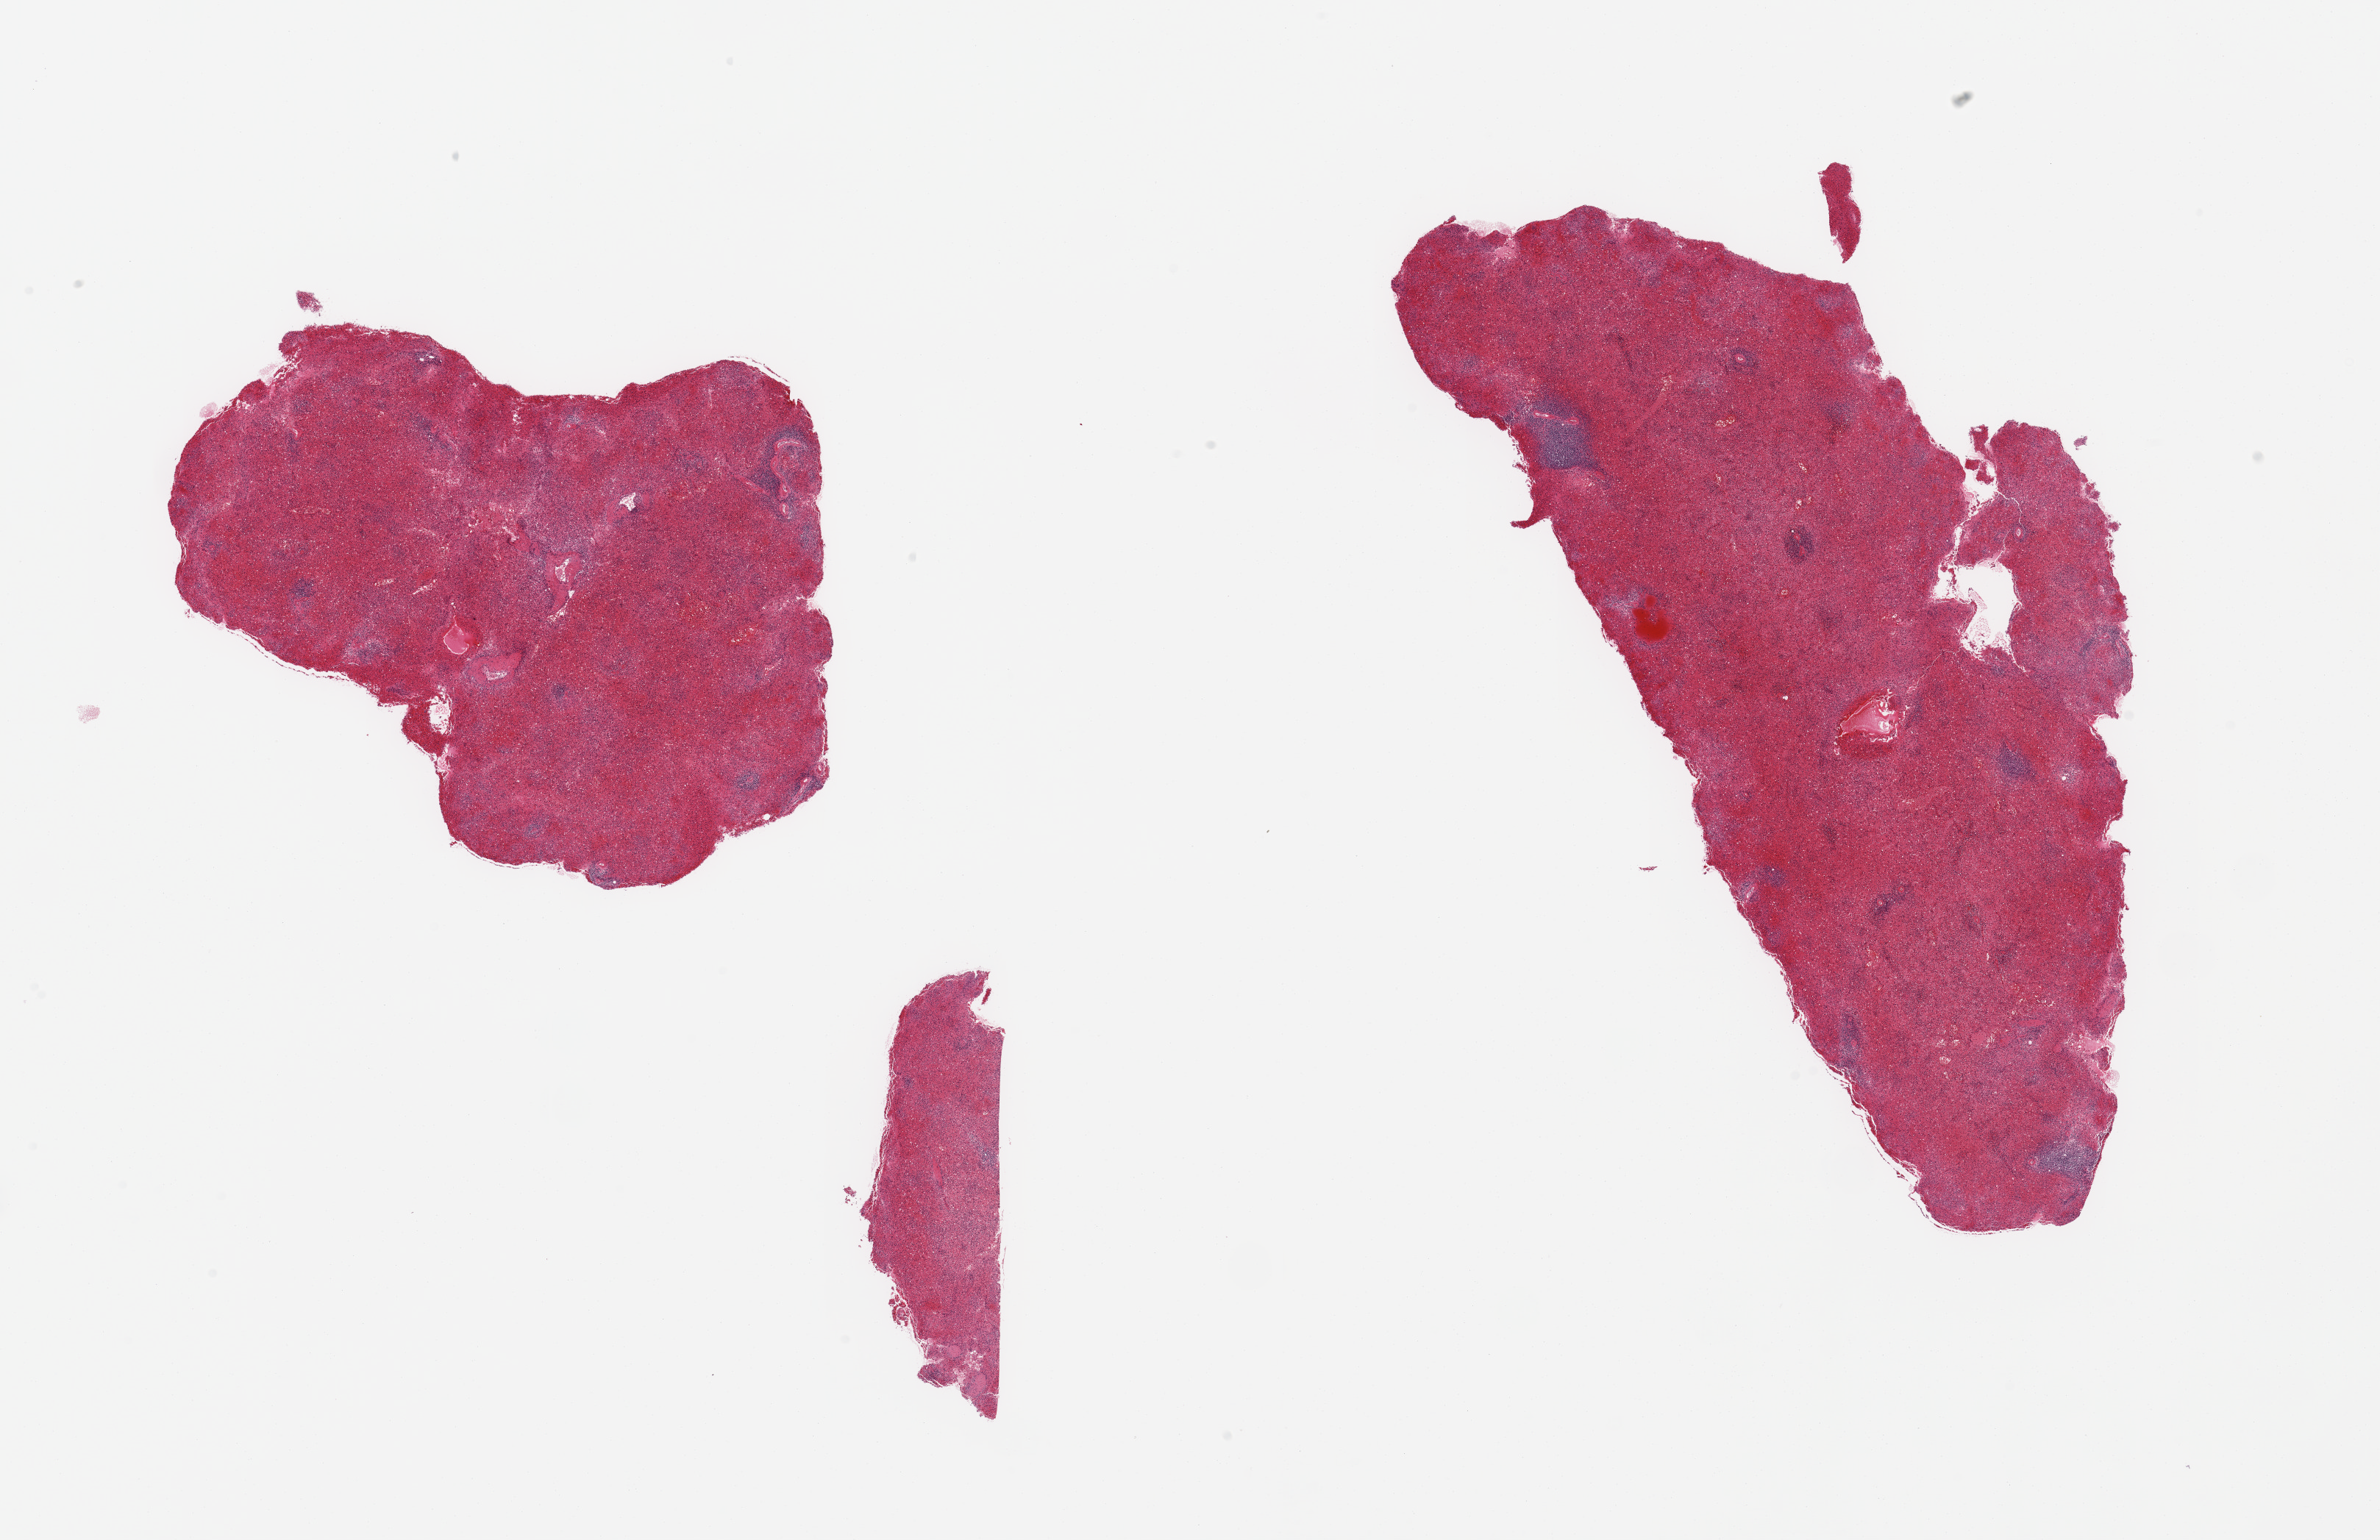
Whole-slide image, hematoxylin and eosin (H&E) stain, whole scanned area (about 25.6 x 16.6 mm) shown as a low-resolution overview; PAXgene-fixed paraffin-embedded (PFPE) section; target tissue: spleen; tissue donor sample.
Pathologist's review note for this sample: 2 pieces, moderate congestion.